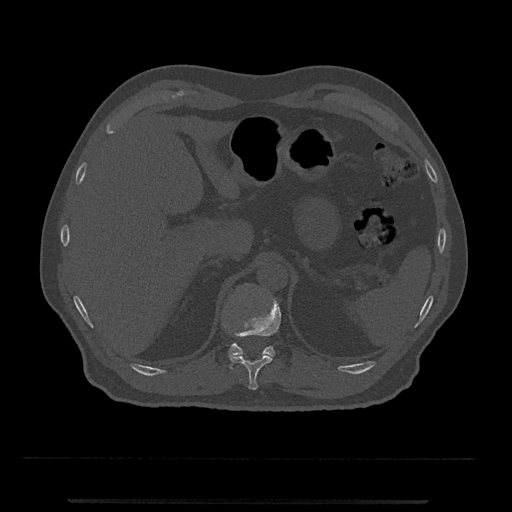
CT including the spine, one axial slice; slice 440 of 797 in the series (ordered by position); 120 kVp; bone window (W 1800 / L 400 HU); 0.5 mm slice thickness; 512 × 512 image matrix. Patient: male, 63 years. Case-level facts recorded for this patient, not image findings: primary cancer: prostate.
Structures marked on this image (semi-automatic segmentation, software-assisted and operator-edited):
- T11 vertebra: box from (x=229, y=298) to (x=281, y=390) px
- T12 vertebra: (x=228, y=343)–(x=275, y=369)